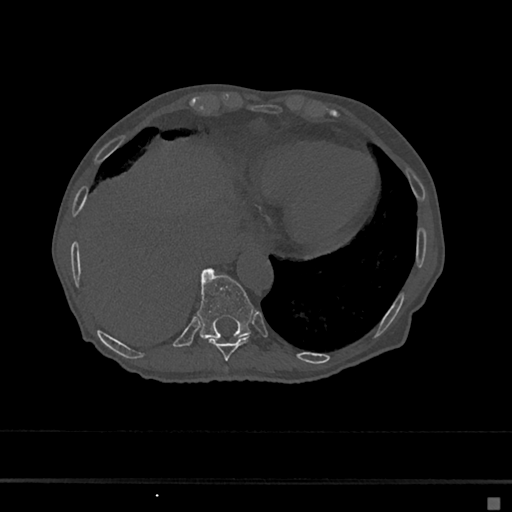
CT including the spine, one axial slice. Slice 246 of 797 in the series (ordered by position). 120 kVp. Bone window (W 1800 / L 400 HU). 0.5 mm slice thickness. 512 × 512 image matrix, field of view 360 × 360 mm. Patient: female, 68 years. From the clinical record (not read from this slice): primary cancer: renal.
Outlined on this slice (semi-automatically segmented with operator editing):
- T10 vertebra: bounding box (x1, y1, x2, y2) in pixels: (197, 269, 253, 339)
- T8 vertebra: (225, 367, 228, 371)
- T9 vertebra: (208, 336, 250, 361)